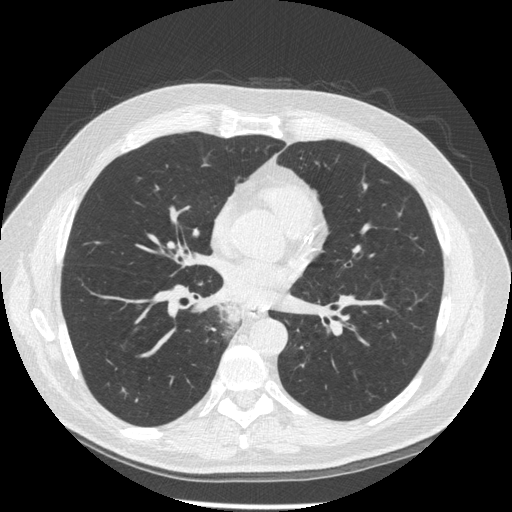
Low-dose screening chest CT, axial slice; third screening round (two years after baseline); lung window (W 1500 / L -600 HU); 1.25 mm slice thickness; slice 91 of 181 in the series; 512 × 512 image matrix, field of view 370 × 370 mm. Male participant, aged 61 years at enrolment. Former smoker at enrolment.
Expert-annotated lung lesion, bounding box <200,297,255,351> (left, top, right, bottom; pixels). No non-calcified nodule or mass ≥4 mm was recorded by the screening reader at this exam. Official screen result: positive, other.